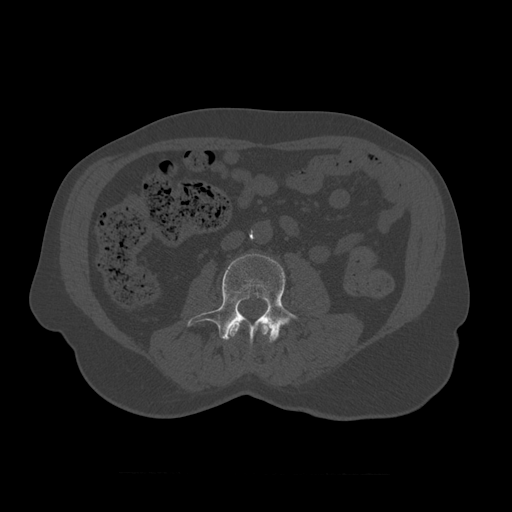
CT including the spine, one axial slice. Slice 306 of 450 in the series (ordered by position). Reconstruction kernel STANDARD. Bone window (W 1800 / L 400 HU). 1.25 mm slice thickness. 512 × 512 image matrix, field of view 405 × 405 mm. Patient age 75 years. From the clinical record (not read from this slice): primary cancer: prostate.
Structures marked on this image (semi-automatic segmentation, software-assisted and operator-edited):
- L2 vertebra: bounding box (x1, y1, x2, y2) in pixels: (230, 321, 271, 338)
- L3 vertebra: (187, 254, 298, 345)